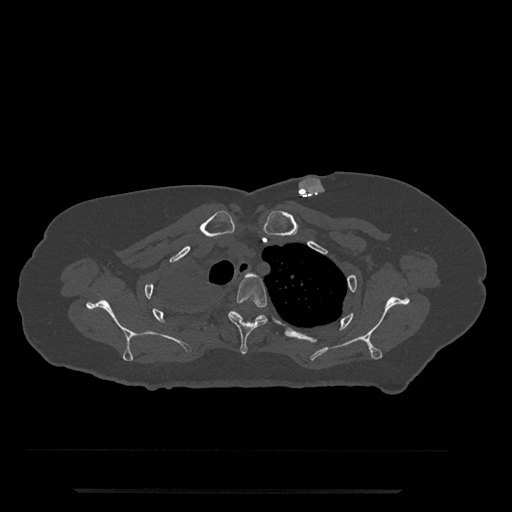
CT including the spine, one axial slice; position 623 of 797 along the scan axis; reconstruction kernel Br40s/3; bone window (W 1800 / L 400 HU); 512 × 512 image matrix, field of view 440 × 440 mm. Female patient, age 51 years. From the clinical record (not read from this slice): primary cancer: neuro.
Outlined on this slice (semi-automatically segmented with operator editing):
- T3 vertebra: bounding box <228,273,268,354> (left, top, right, bottom; pixels)
- T4 vertebra: <212,311,278,334>